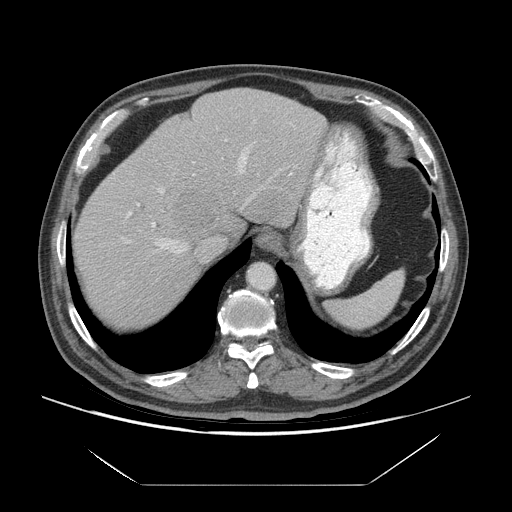
Contrast-enhanced abdominal CT (liver protocol), one axial slice; slice 54 of 75 in the series (ordered by position); 140 kVp; soft-tissue window (W 400 / L 40 HU); 2.5 mm slice thickness; 512 × 512 image matrix, field of view 420 × 420 mm. From the clinical record (not read from this slice): diagnosis: hepatocellular carcinoma (patient treated with transarterial chemoembolisation; whether this scan precedes or follows treatment is not stated here); TNM stage (as recorded): Stage-I; Child-Pugh class: A.
Annotated regions visible in this slice (semi-automatically segmented with operator editing):
- abdominal aorta: bounding box [x1, y1, x2, y2] px = [248, 264, 273, 290]
- liver parenchyma outside the tumour (the mass and vessels are separate outlines, so this box may not span the whole liver): [72, 88, 326, 326]
- mass: [172, 187, 220, 229]
- liver vessels: [126, 139, 281, 254]